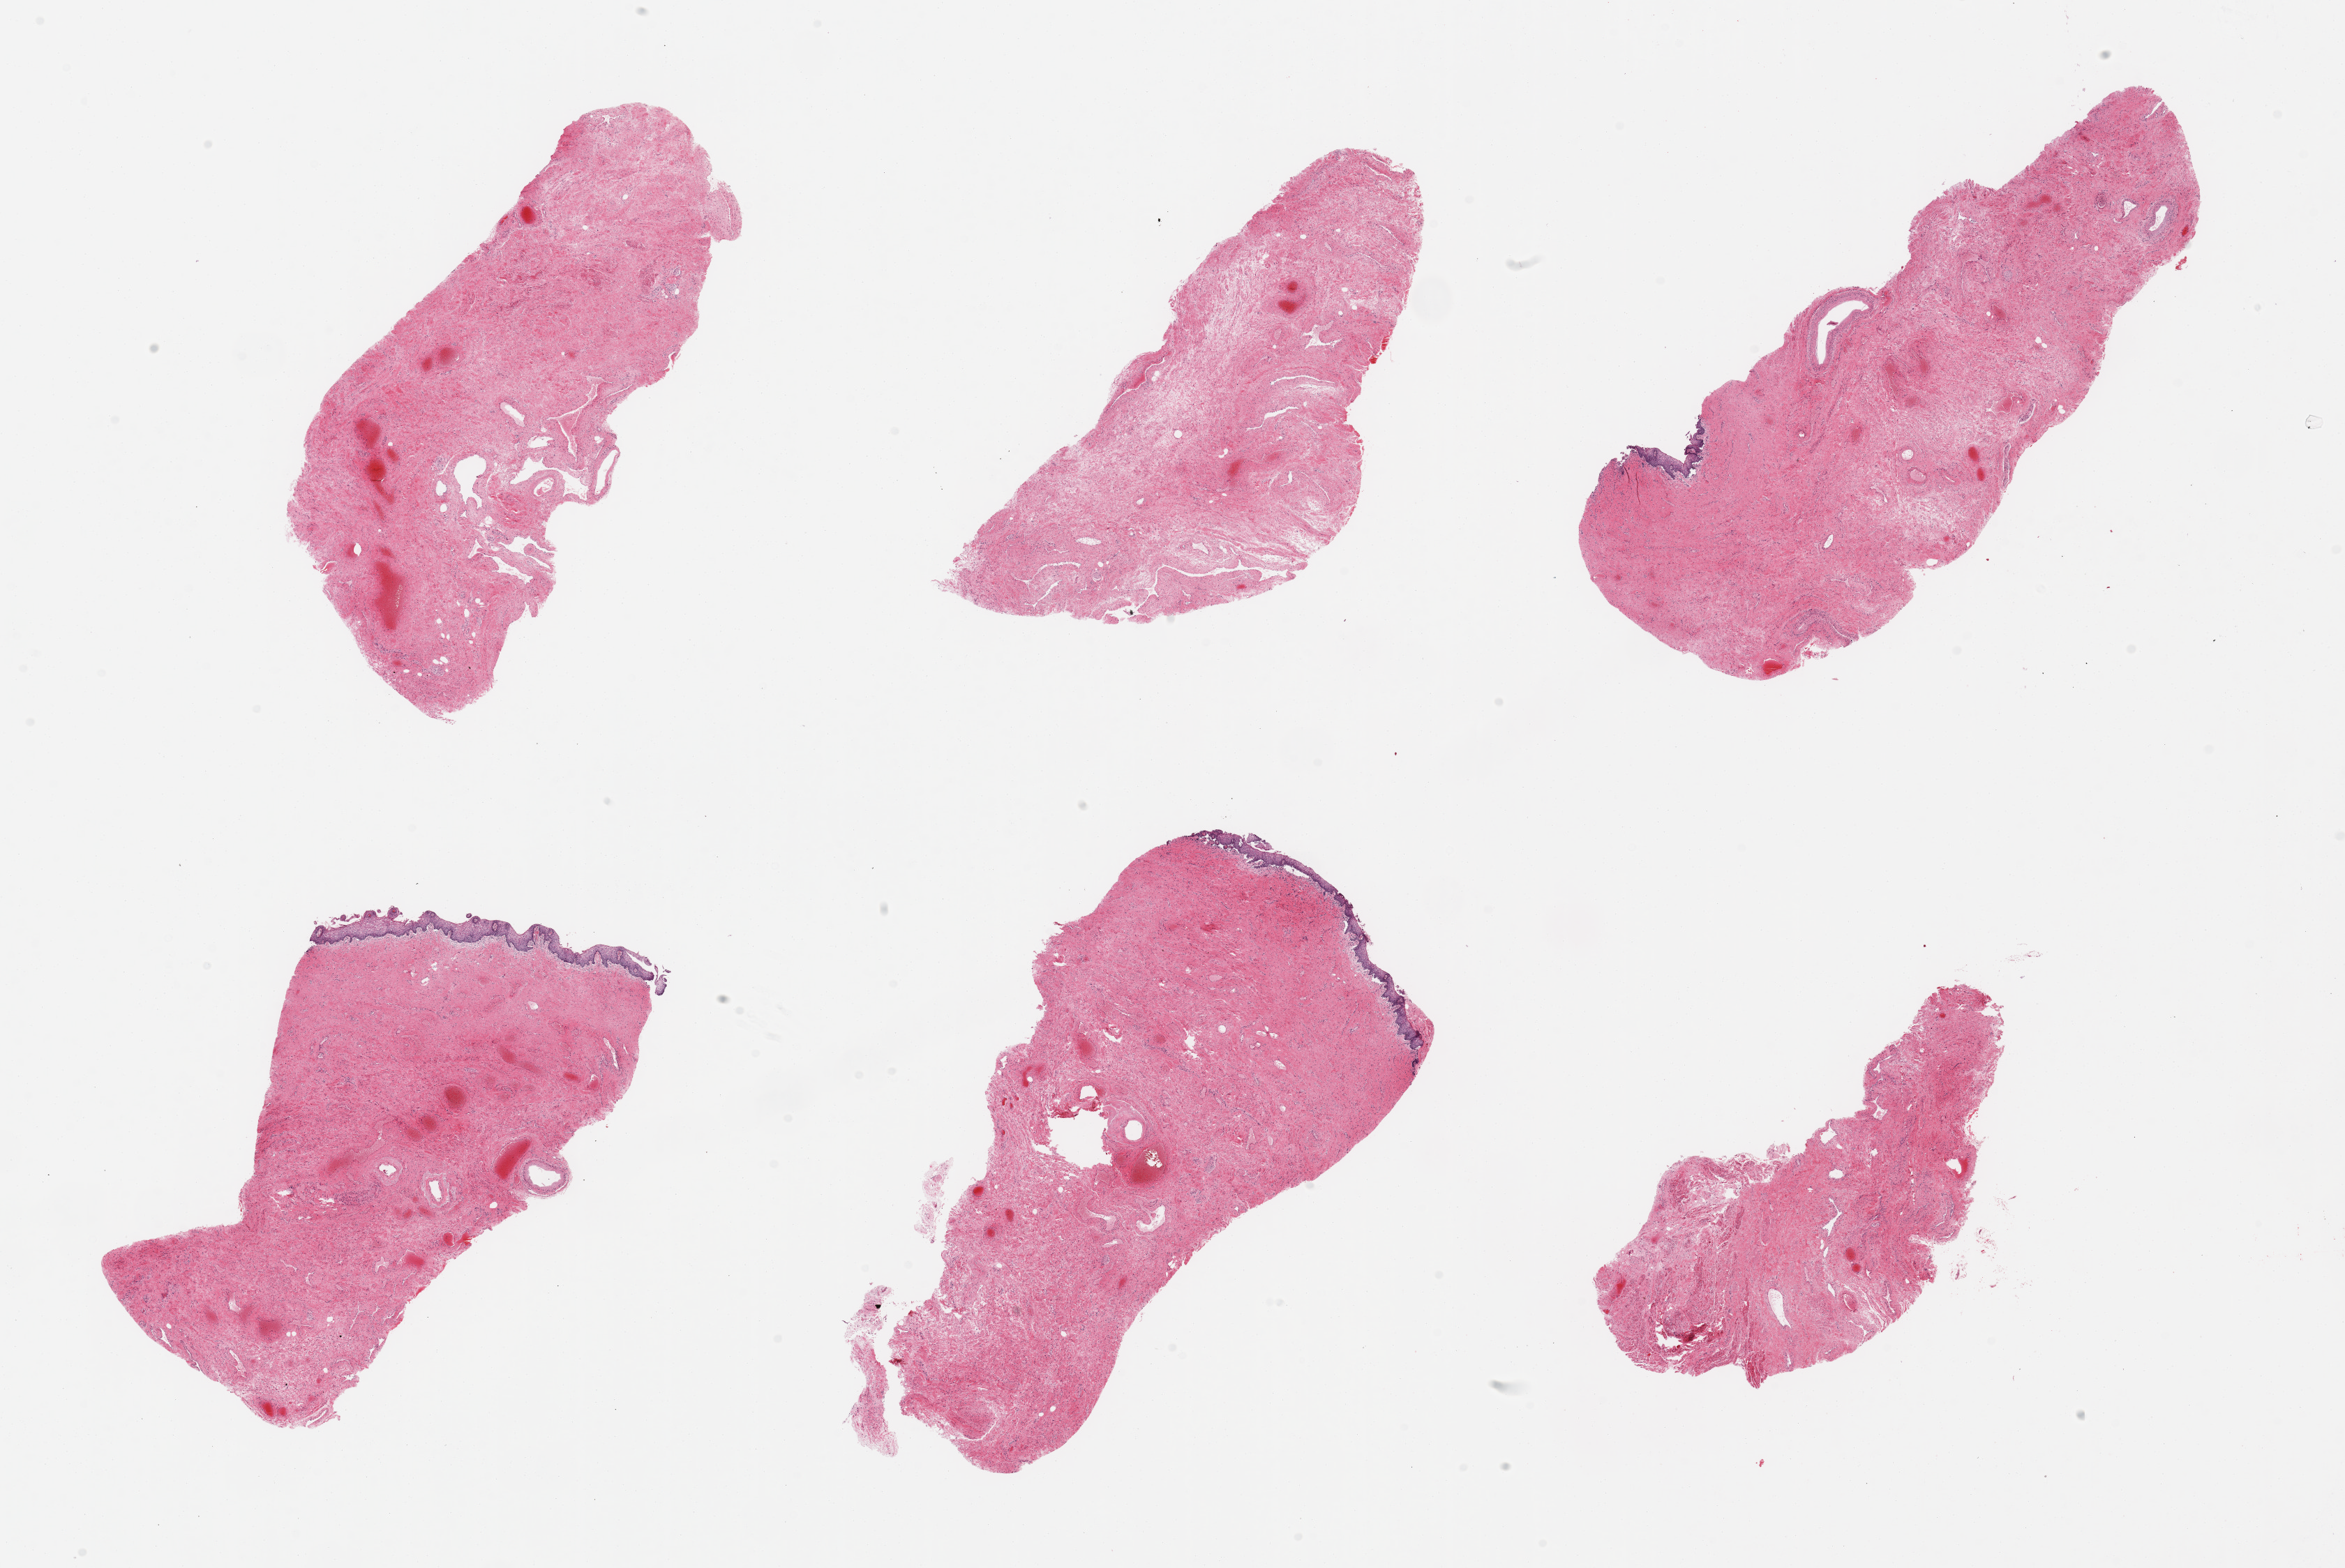
Whole-slide image, haematoxylin and eosin stain, brightfield, a low-resolution overview of the entire scanned area, about 26.6 x 17.8 mm. PAXgene-fixed paraffin-embedded (PFPE) section. Section of vagina (target tissue). Donor tissue sample. Donor sex: female.
Reviewer comment on this tissue sample: 6 pieces, squamous mucosa up to ~0.2mm.